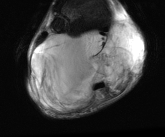
MRI of an extremity soft-tissue mass, one axial slice; position 20 of 81 along the scan axis; T2-weighted fat-saturated; MR volume resampled by the dataset authors to the PET/CT grid (not the native acquisition matrix); 3.27 mm slice thickness; 165 × 137 image matrix. Male patient. From the clinical record (not read from this slice): histological type: liposarcoma - round cell; grade: high; site of the primary tumour: right calf.
Outlined on this slice (expert contour drawn on MRI and transferred to this co-registered scan by the dataset authors):
- gross tumour volume (mass): bounding box (x1, y1, x2, y2) in pixels: (30, 23, 140, 113)